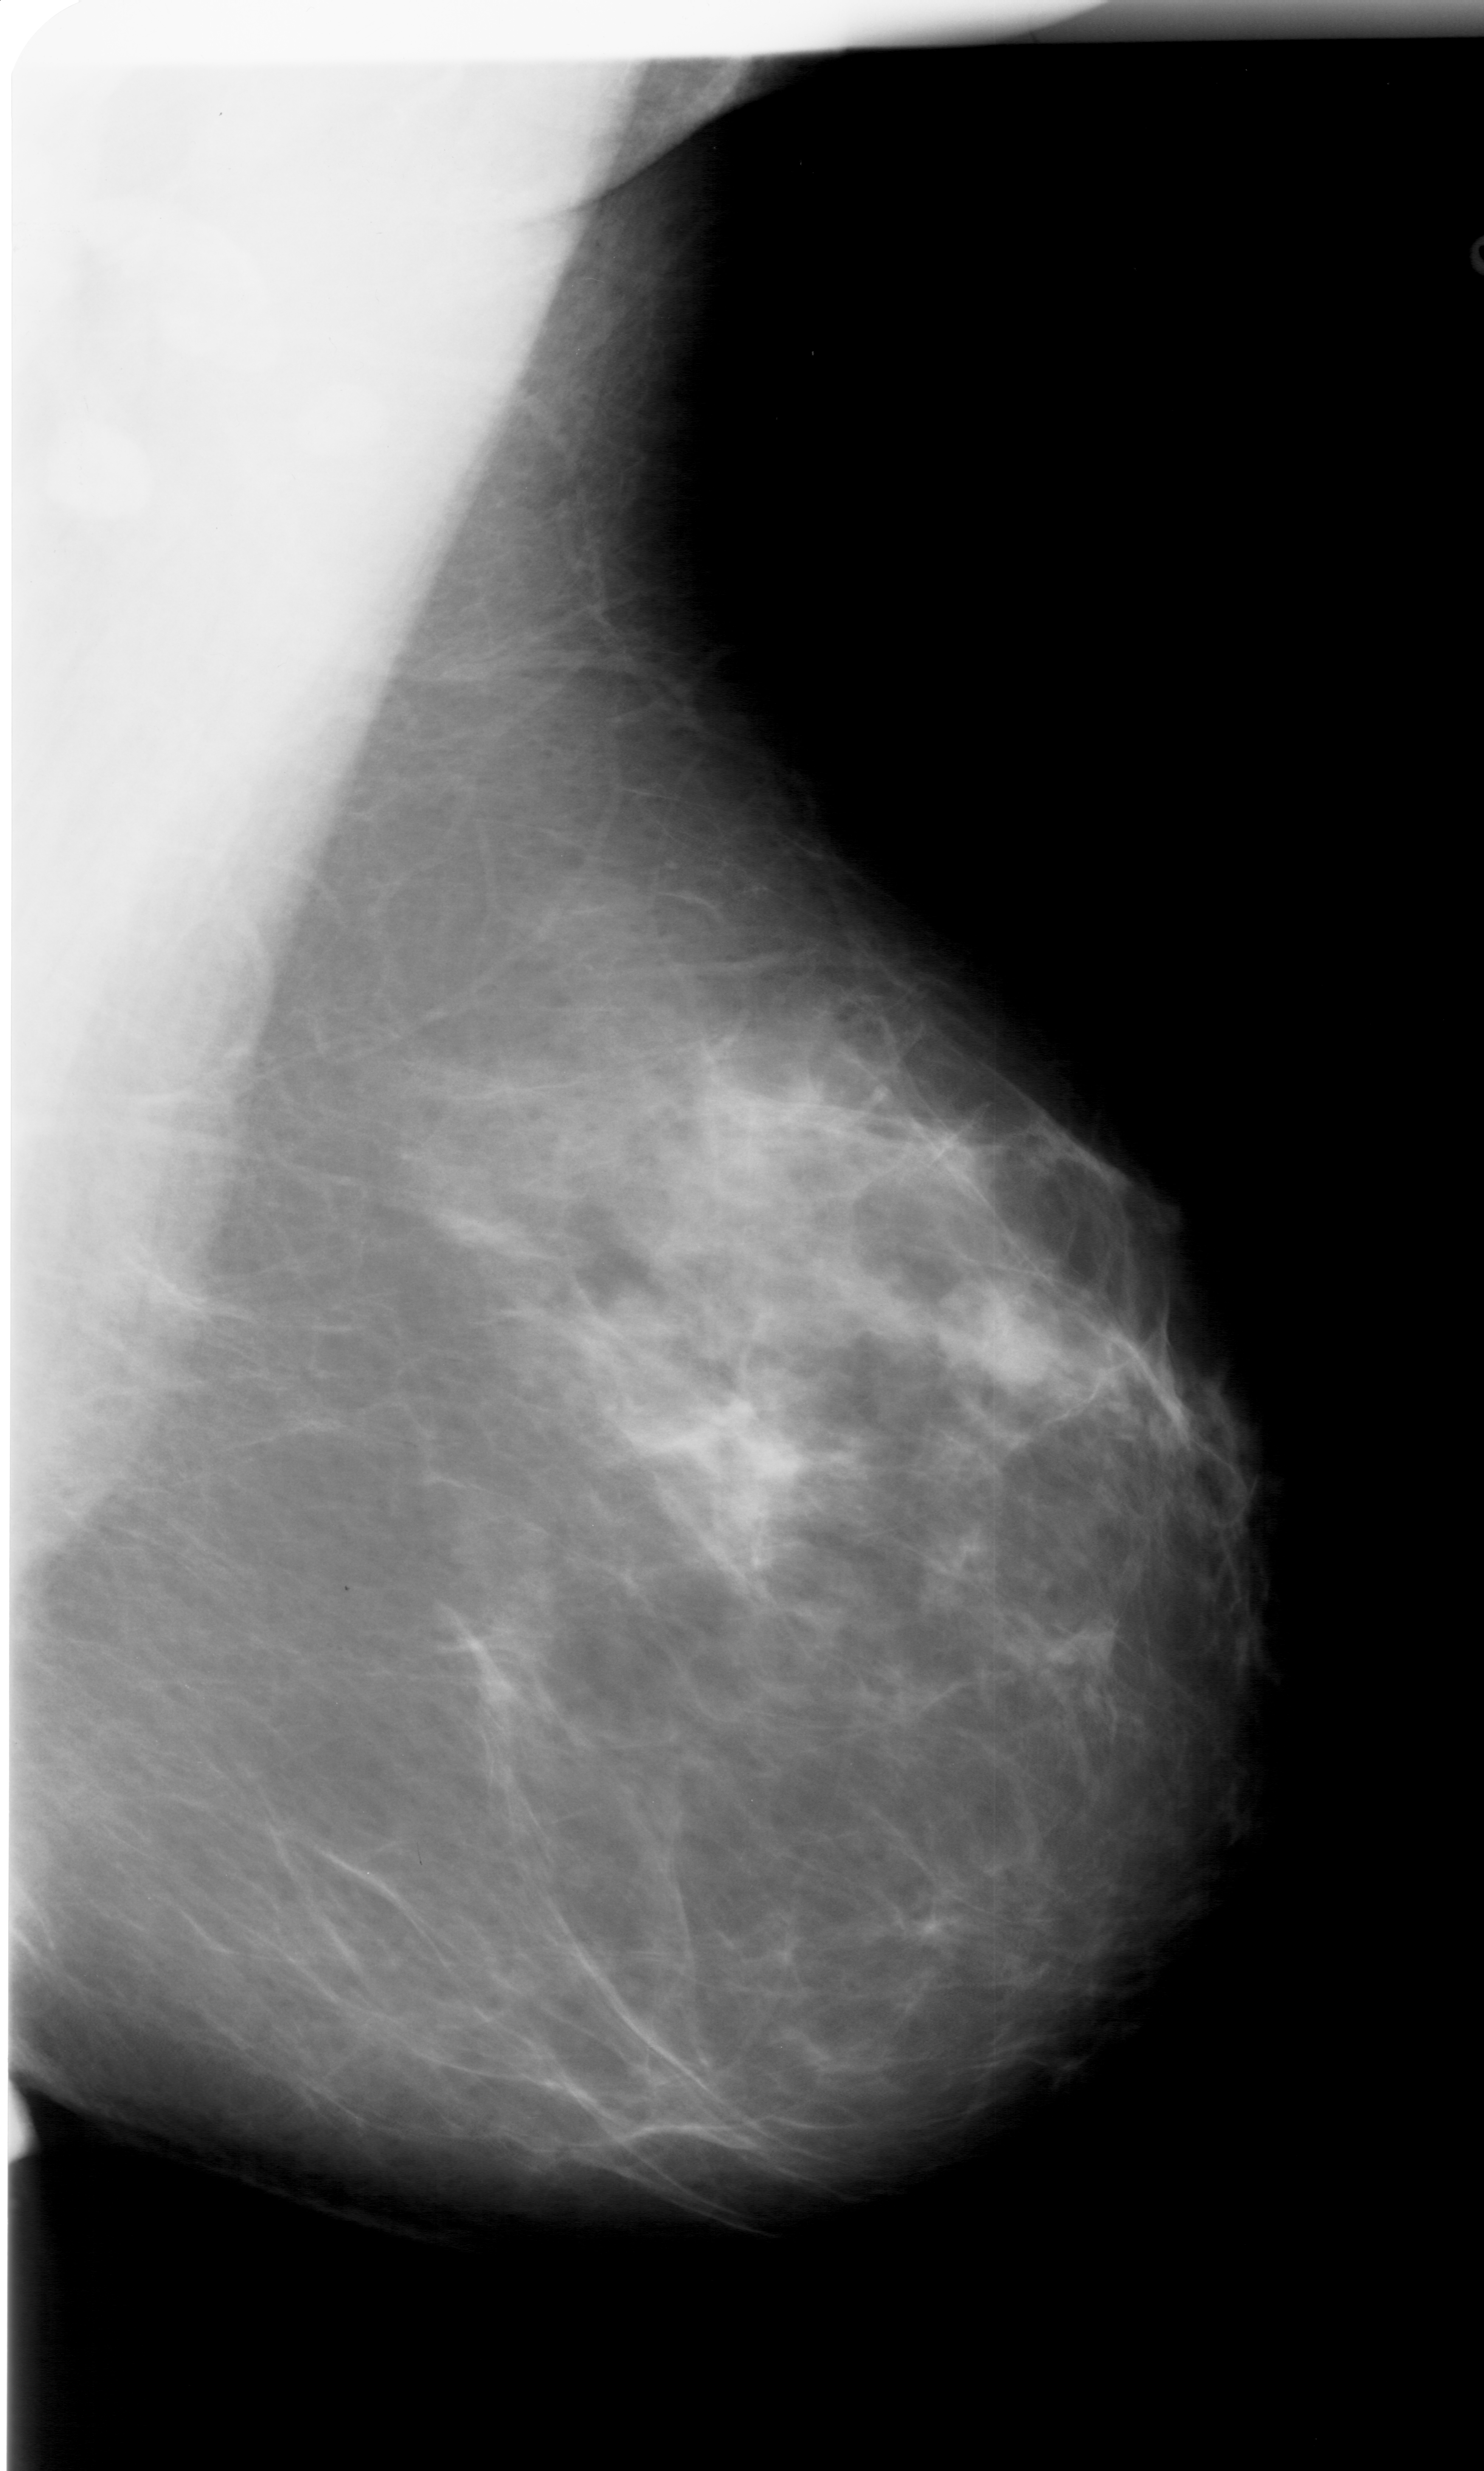
Digitized screen-film mammogram; right breast; mediolateral oblique (MLO) view; BI-RADS breast density category 2 (scale 1–4); 1484 × 2471 image matrix.
Expert-marked regions of interest on this film, with their recorded descriptors:
- mass, shape oval, margins circumscribed; BI-RADS assessment category 3; pathology (as recorded): benign: bounding box <949,1278,1052,1387> (left, top, right, bottom; pixels)